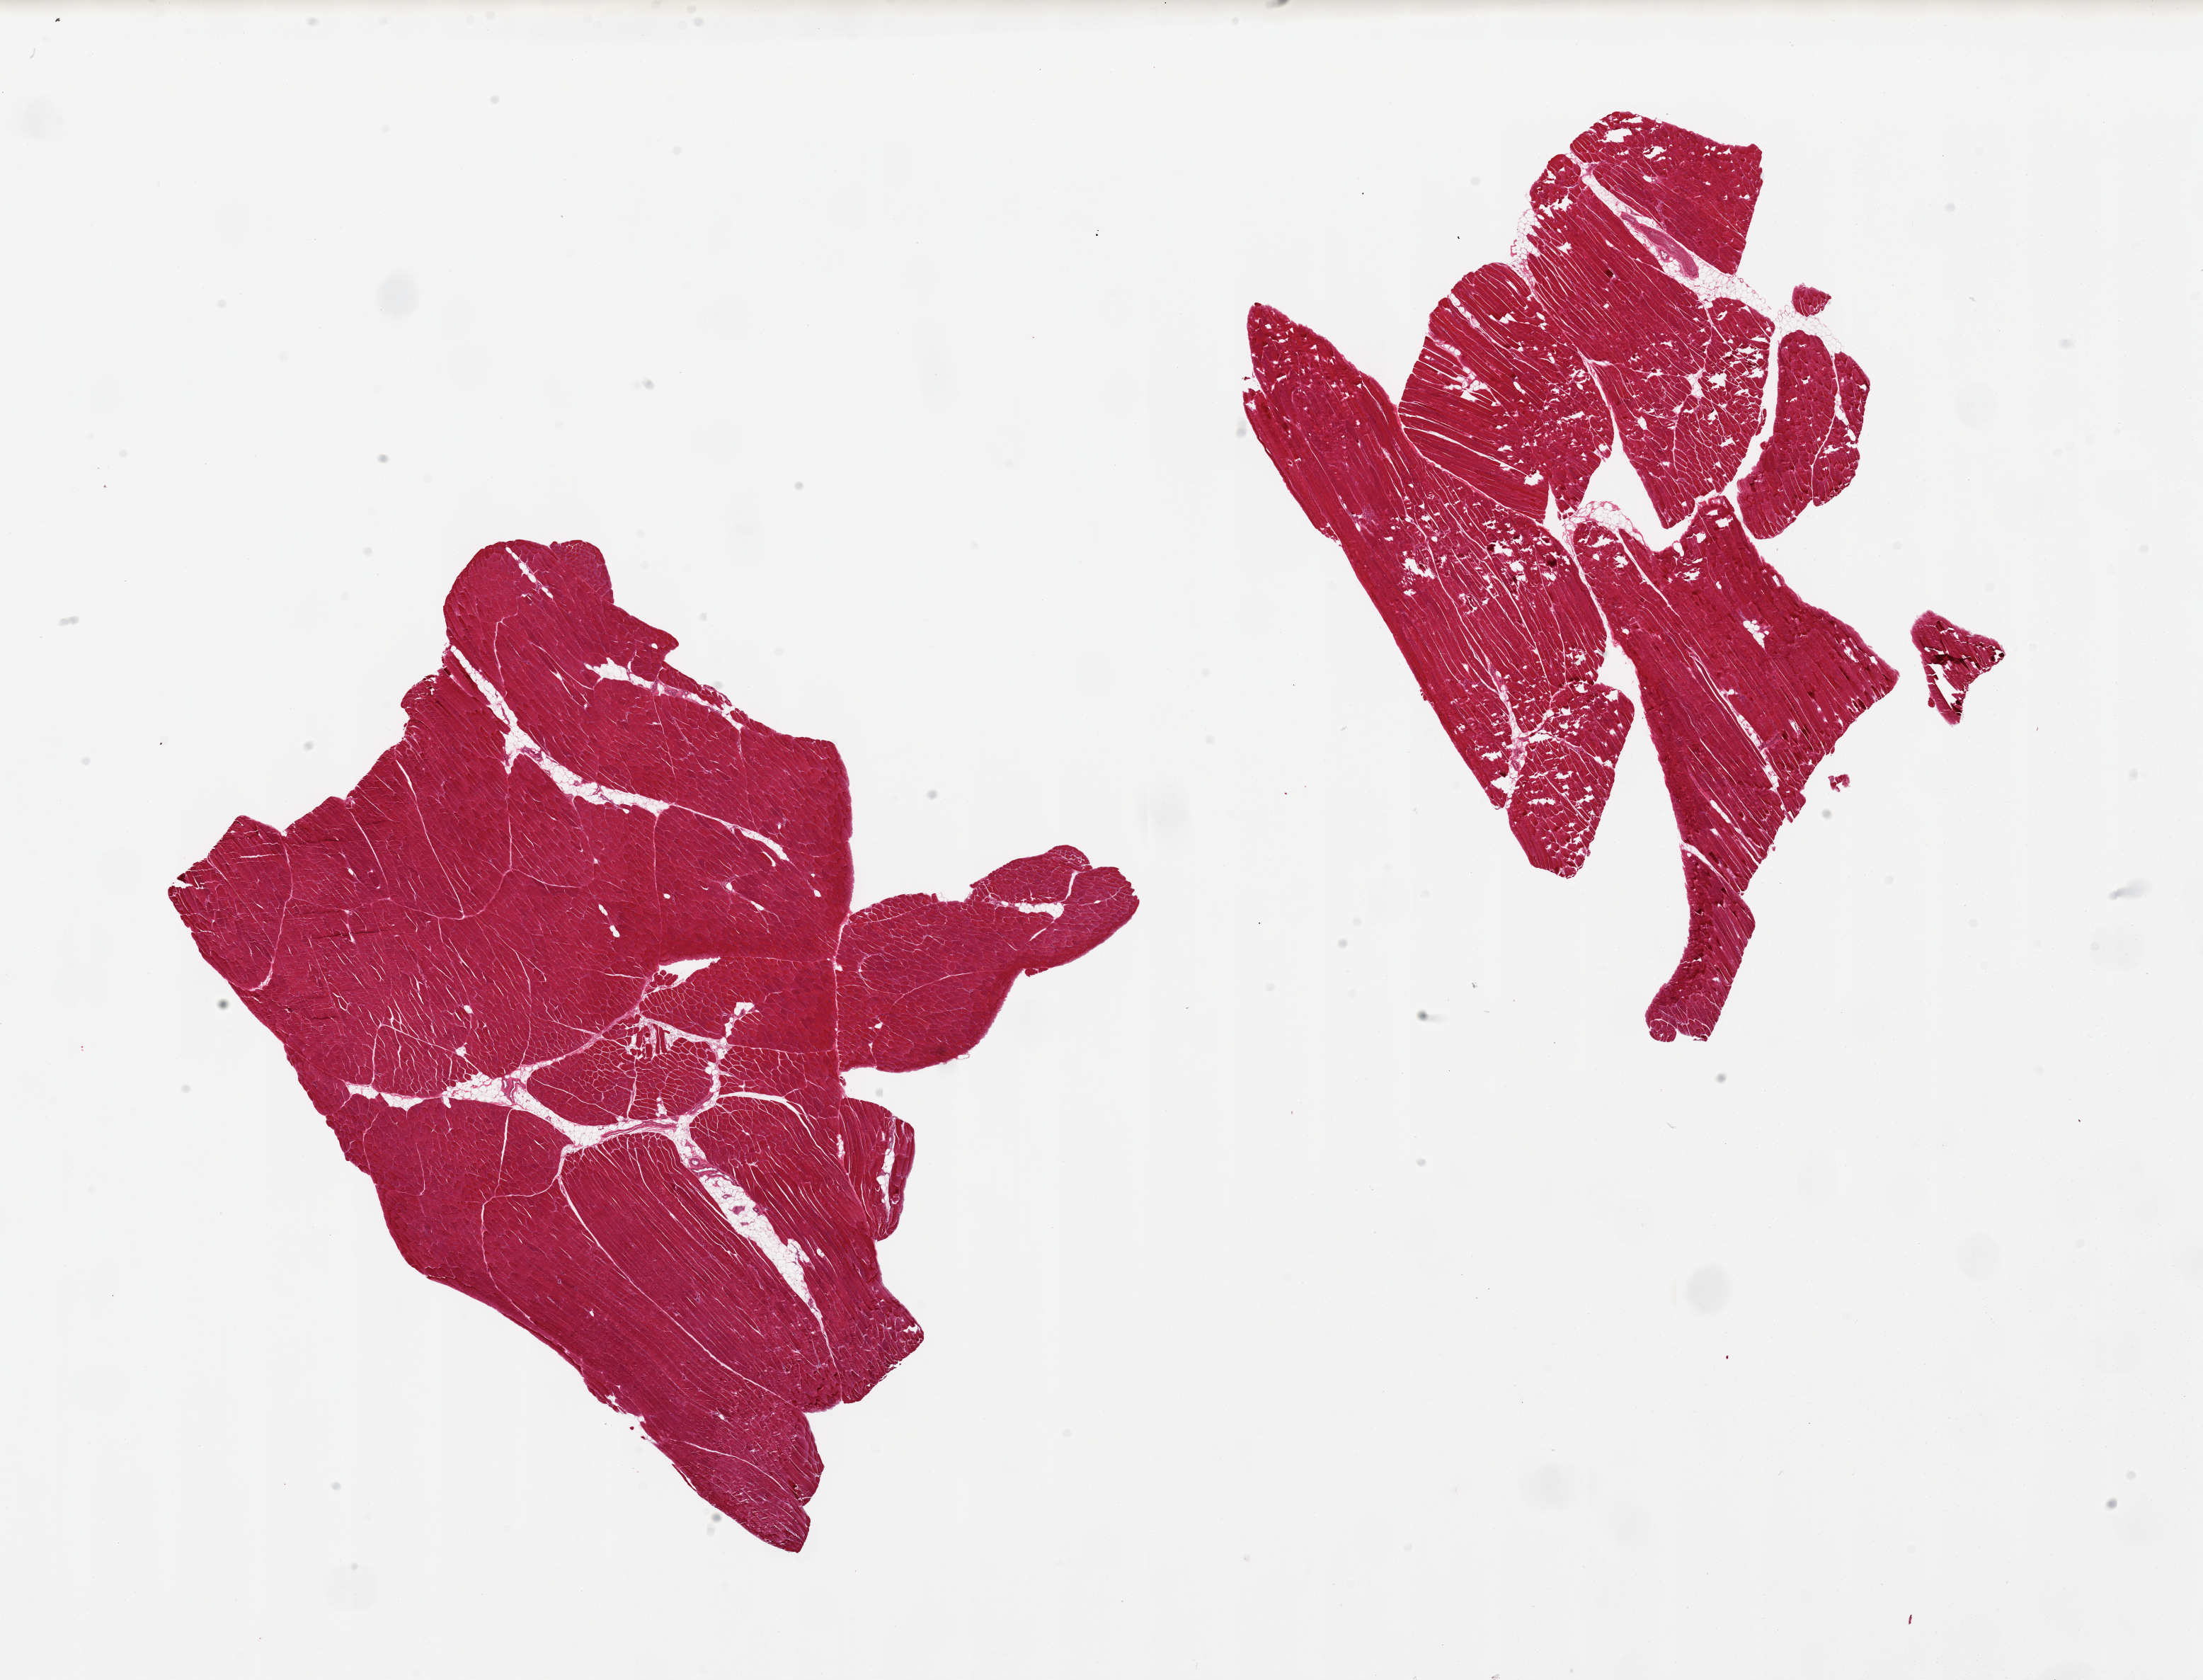
Haematoxylin and eosin whole-slide image, brightfield — a low-resolution overview of the entire scanned area, about 24.6 x 18.8 mm, PAXgene-fixed, paraffin-embedded tissue, target tissue: skeletal muscle, tissue donor sample. Donor: male.
• review note (as recorded): 2 pieces, minimal interstitial fat